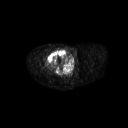
FDG PET of an extremity soft-tissue mass (from a PET/CT study), one axial slice. Position 267 of 311 along the scan axis. 3.27 mm slice thickness. 128 × 128 image matrix, field of view 700 × 700 mm. Patient: male, 50 years. From the clinical record (not read from this slice): histological type: undifferentiated - pleiomorphic; grade: high; site of the primary tumour: right thigh.
Outlined on this slice (expert contour drawn on MRI and transferred to this co-registered scan by the dataset authors):
- gross tumour volume including surrounding oedema: bounding box <46,48,67,68> (left, top, right, bottom; pixels)
- gross tumour volume (mass): <46,48,67,68>